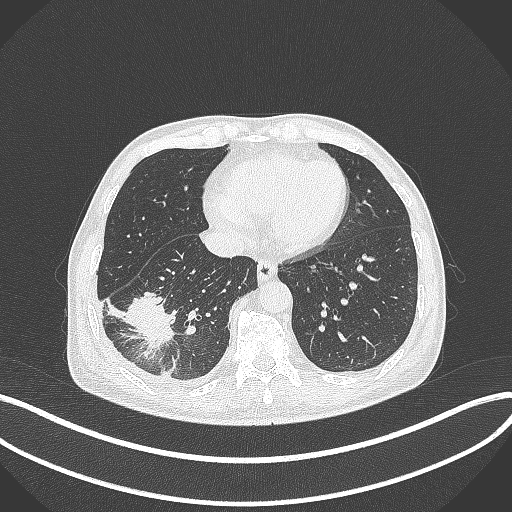
Chest CT, one axial slice; 120 kVp; lung window (W 1500 / L -600 HU); 1 mm slice thickness; 512 × 512 image matrix, field of view 400 × 400 mm. Patient: male, 64 years. Case-level facts recorded for this patient, not image findings: clinical TNM (as recorded): T3 N0 M0; histopathological grade: G2-3.
Outlined on this slice (rectangle marked by the reading radiologist):
- lung tumour (recorded histology: adenocarcinoma): box from (x=123, y=289) to (x=176, y=352) px